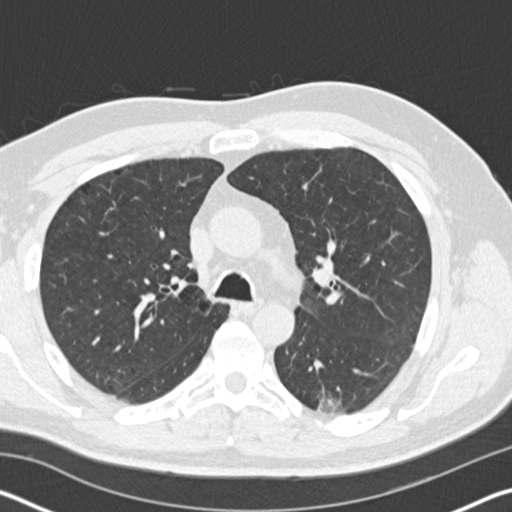
Low-dose screening chest CT, one axial slice; position 115 of 178 along the scan axis; reconstruction kernel B30f; 120 kVp; lung window (W 1500 / L -600 HU); 2 mm slice thickness; 512 × 512 image matrix, field of view 340 × 340 mm.
Annotated regions visible in this slice (expert manual segmentation):
- lesion 1 (tumor, lower lobe of left lung): bounding box (x1, y1, x2, y2) in pixels: (317, 399, 340, 412)